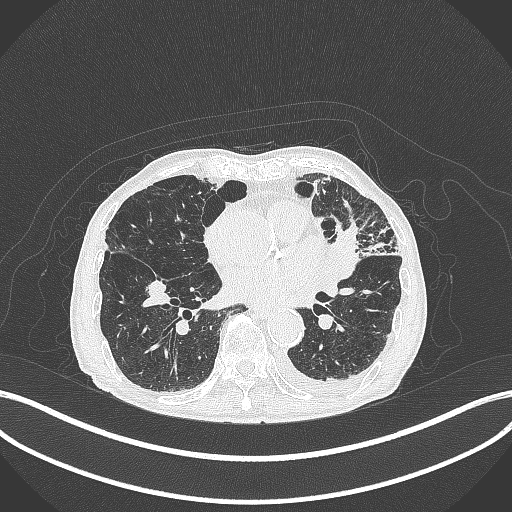
Chest CT, one axial slice. Position 163 of 385 along the scan axis. Reconstruction kernel B70f. 120 kVp. Lung window (W 1500 / L -600 HU). 1 mm slice thickness. 512 × 512 image matrix, field of view 400 × 400 mm. Patient: male, 90 years or older. Case-level facts recorded for this patient, not image findings: clinical TNM (as recorded): T2b N1 M0.
Structures marked on this image (bounding box drawn by a radiologist):
- lung tumour (recorded histology: squamous cell carcinoma): box from (x=326, y=221) to (x=363, y=280) px